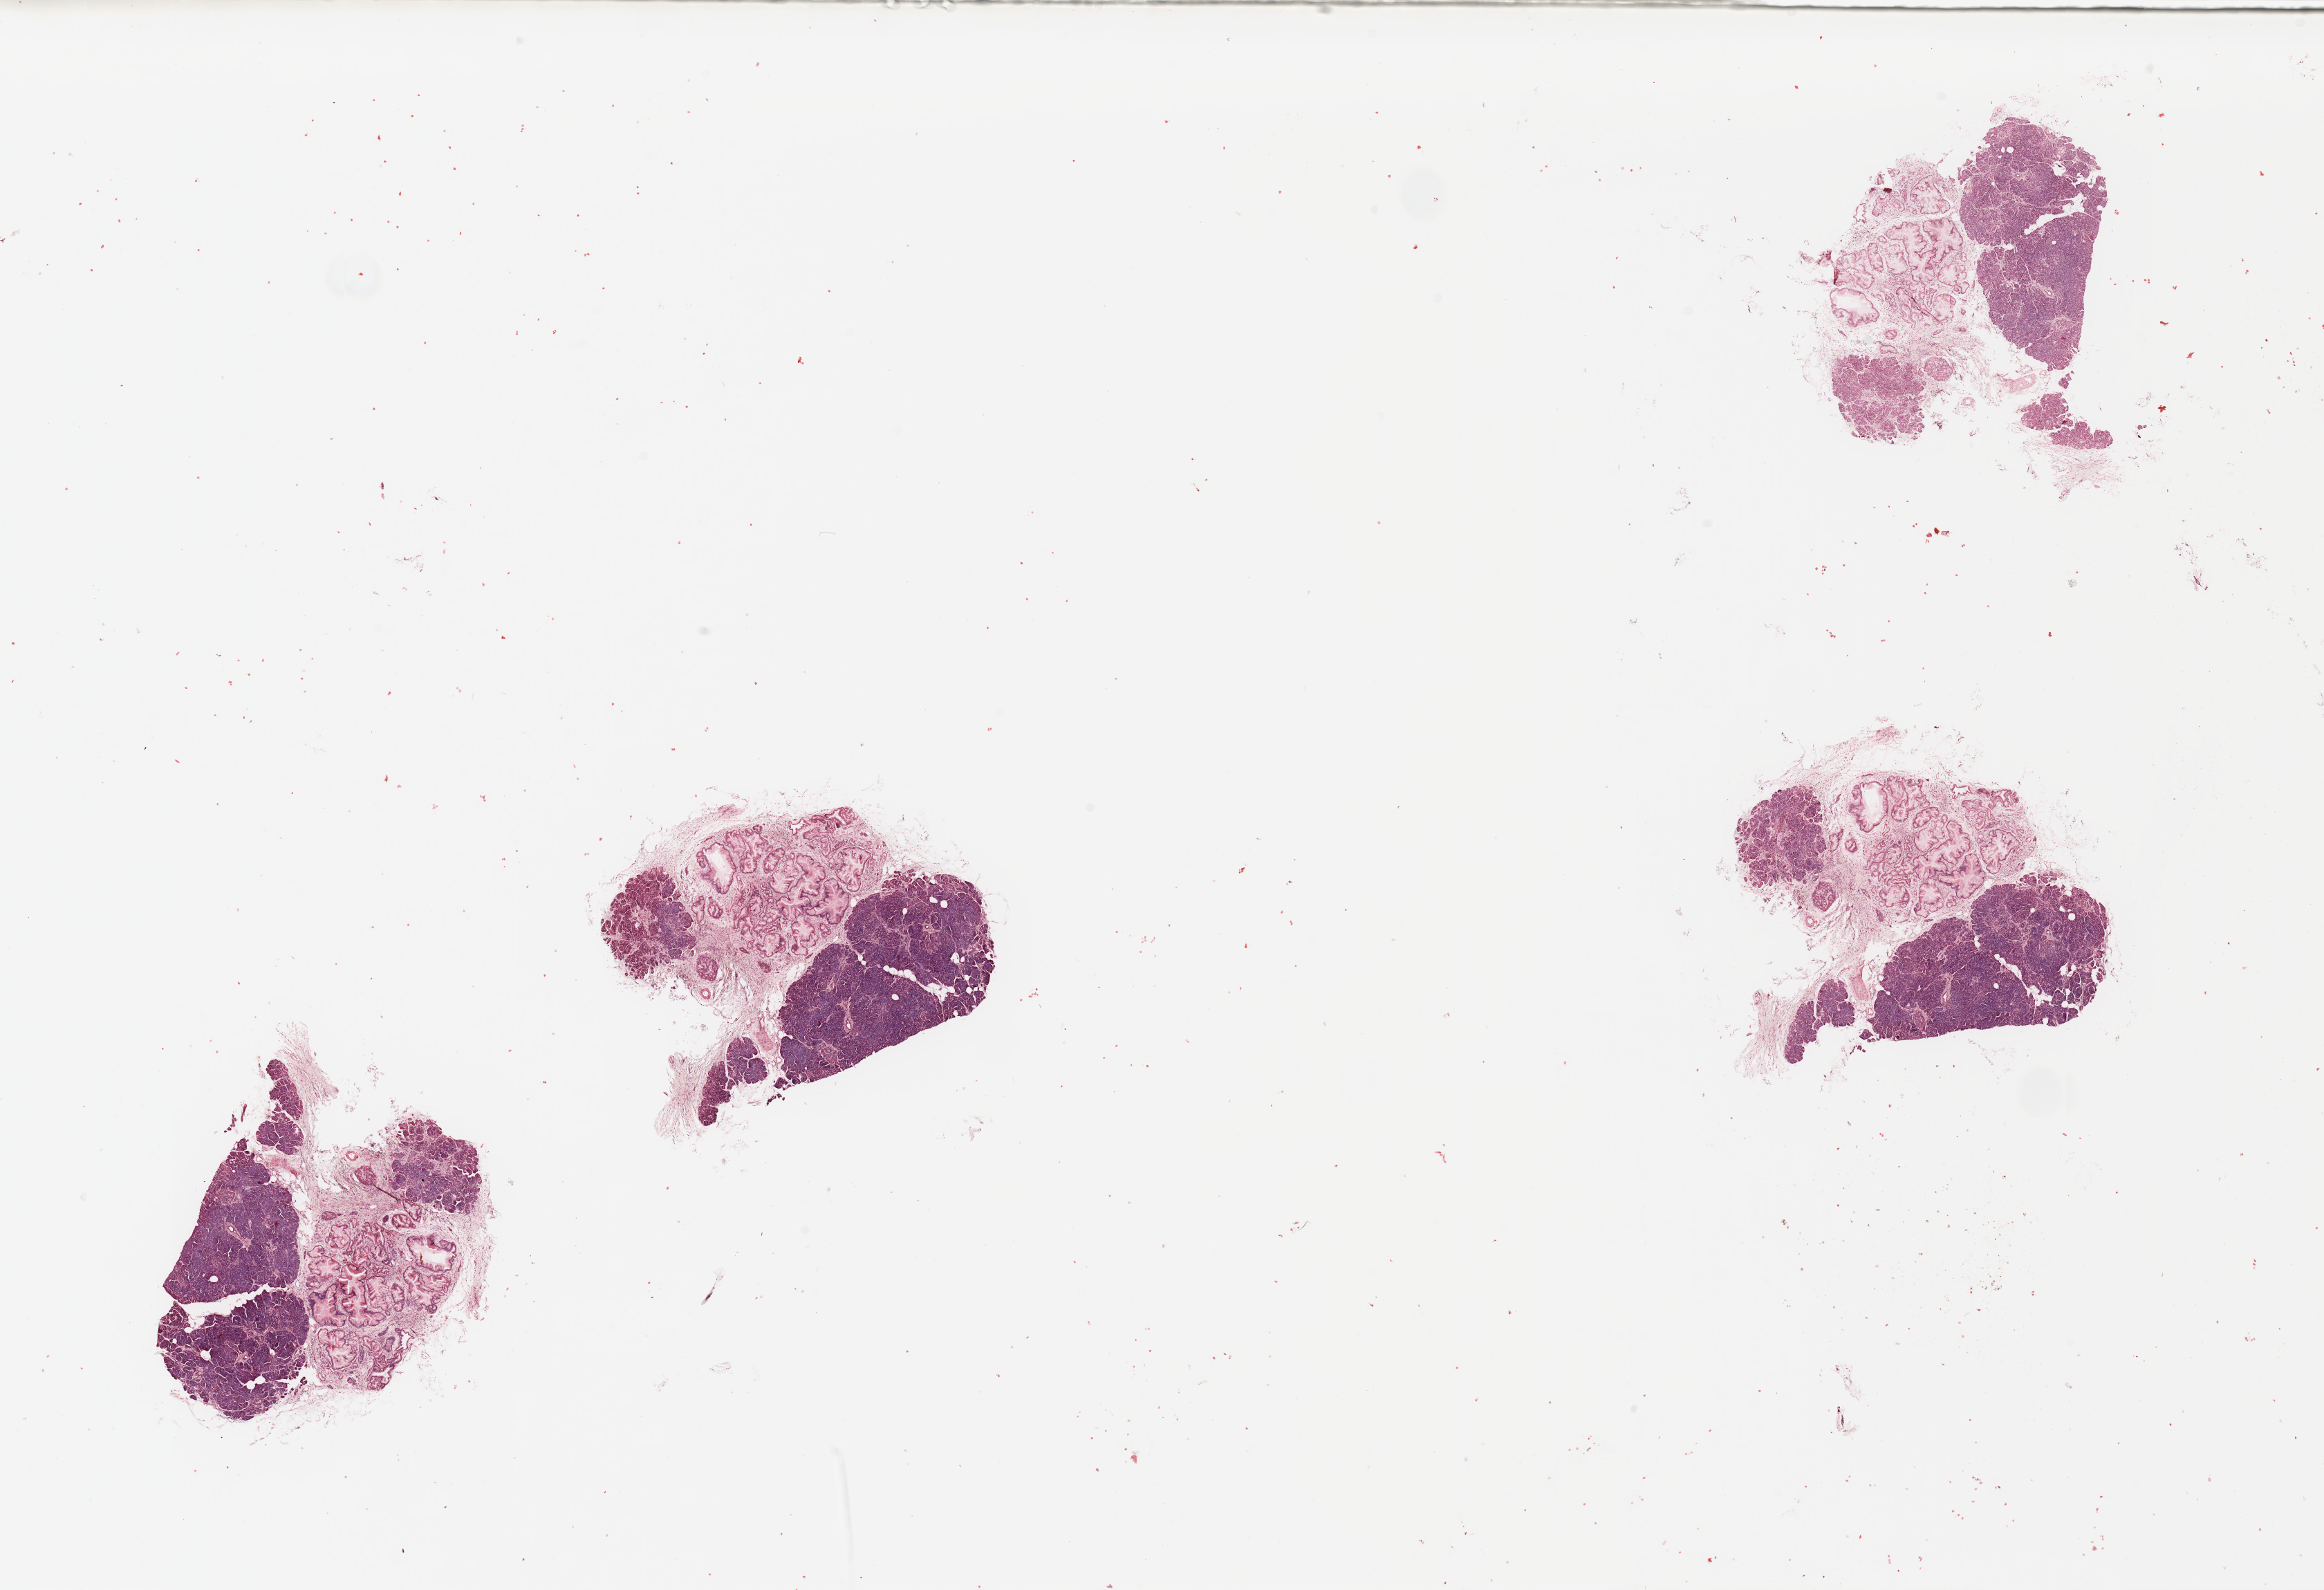
H&E whole-slide image — shown as a low-resolution overview of the whole scanned area (about 26.6 x 18.2 mm), pancreas, normal (non-tumour) tissue. Patient: male, age 56 years.
This section: normal (non-tumour) tissue from the same patient. Patient diagnosis: Infiltrating duct carcinoma, NOS.